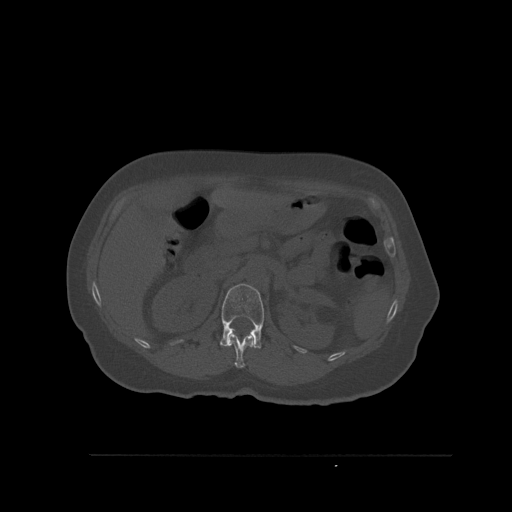
CT including the spine, one axial slice; slice 272 of 527 in the series (ordered by position); bone window (W 1800 / L 400 HU); 512 × 512 image matrix, field of view 470 × 470 mm. Female patient, age 73 years. Case-level facts recorded for this patient, not image findings: primary cancer: breast; vertebrae with lytic lesions (as recorded): L2.
Outlined on this slice (semi-automatic segmentation, software-assisted and operator-edited):
- L1 vertebra: bounding box (x1, y1, x2, y2) in pixels: (220, 283, 264, 349)
- T12 vertebra: (227, 332, 254, 368)